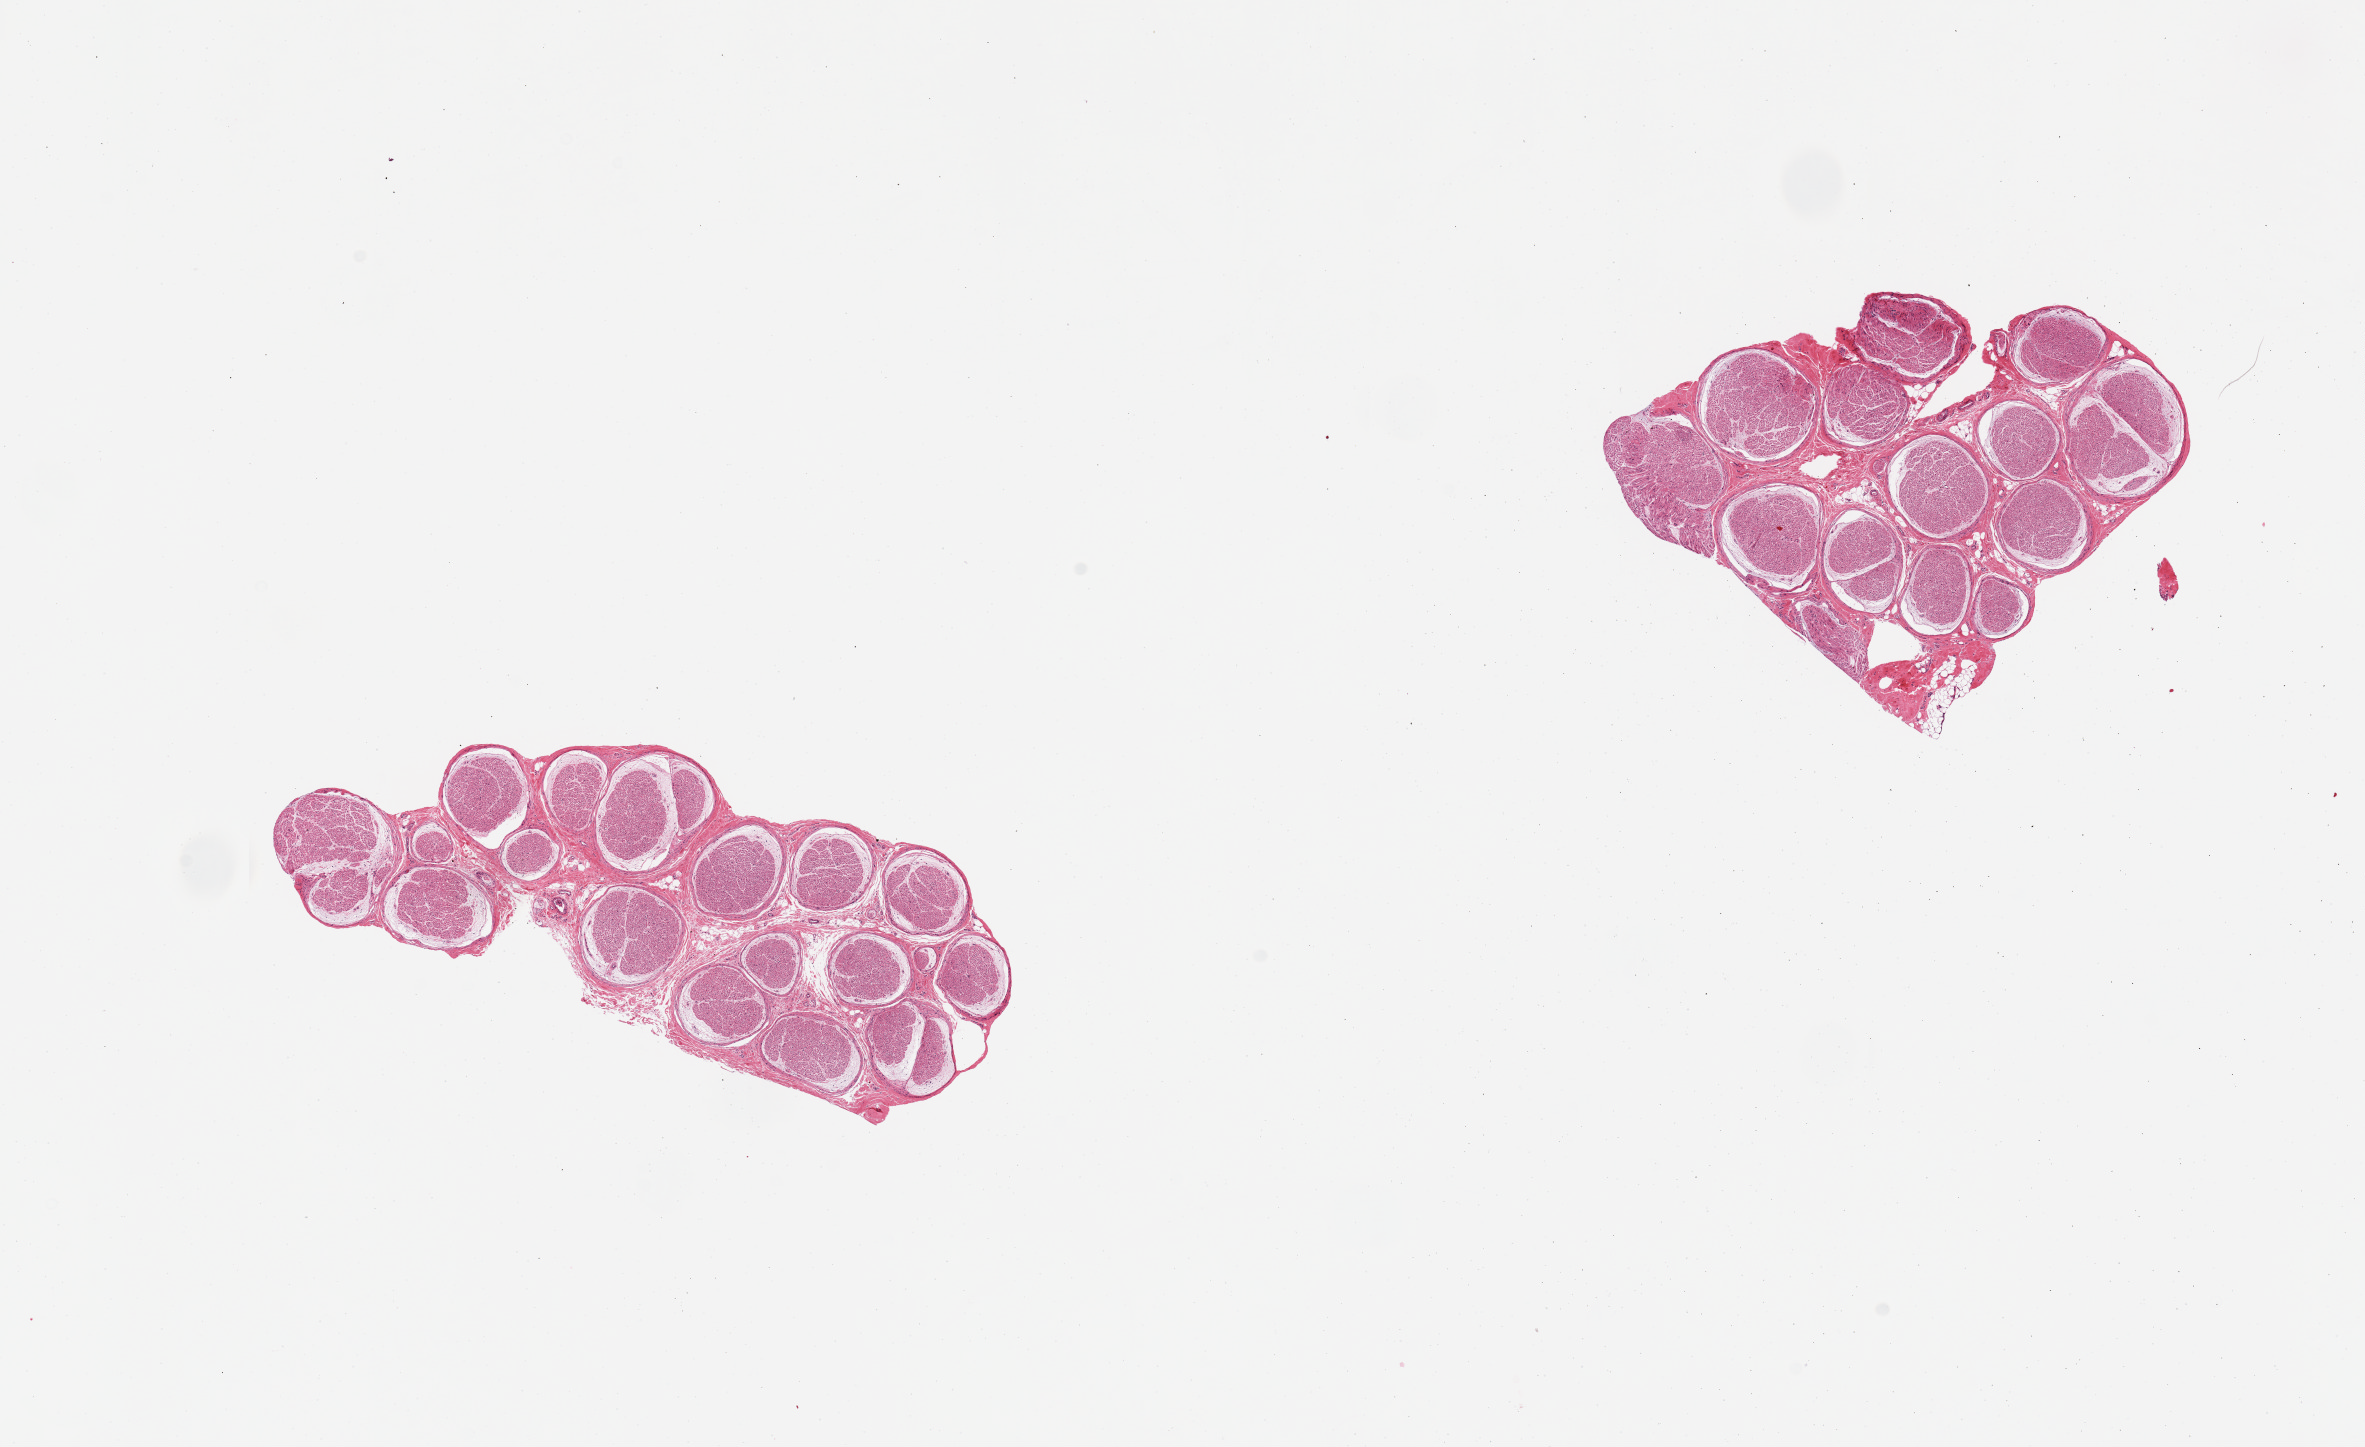
Hematoxylin and eosin (H&E) whole-slide image — a low-resolution overview of the entire scanned area, about 18.7 x 11.4 mm. PAXgene-fixed paraffin-embedded (PFPE) section. Target tissue: tibial nerve. Donor tissue sample. Female donor.
Reviewer comment on this tissue sample: 2 pieces; no extraneous fat.